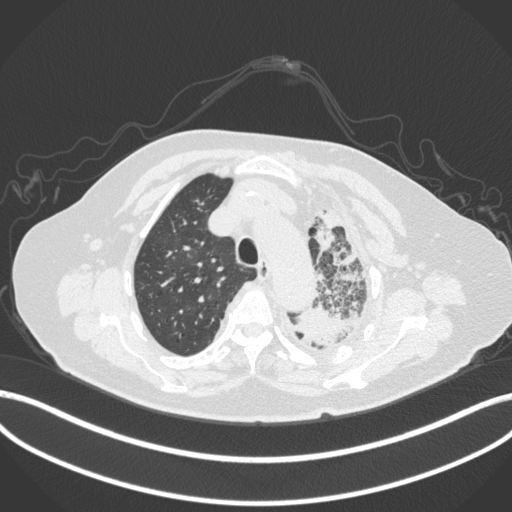
Chest CT, one axial slice; position 306 of 399 along the scan axis; 120 kVp; lung window (W 1500 / L -600 HU); 512 × 512 image matrix, field of view 400 × 400 mm. Patient: female, 75 years. Case-level facts recorded for this patient, not image findings: clinical TNM (as recorded): T3 N3 M1.
Outlined on this slice (rectangle marked by the reading radiologist):
- lung tumour (recorded histology: adenocarcinoma): bounding box (x1, y1, x2, y2) in pixels: (283, 299, 356, 355)